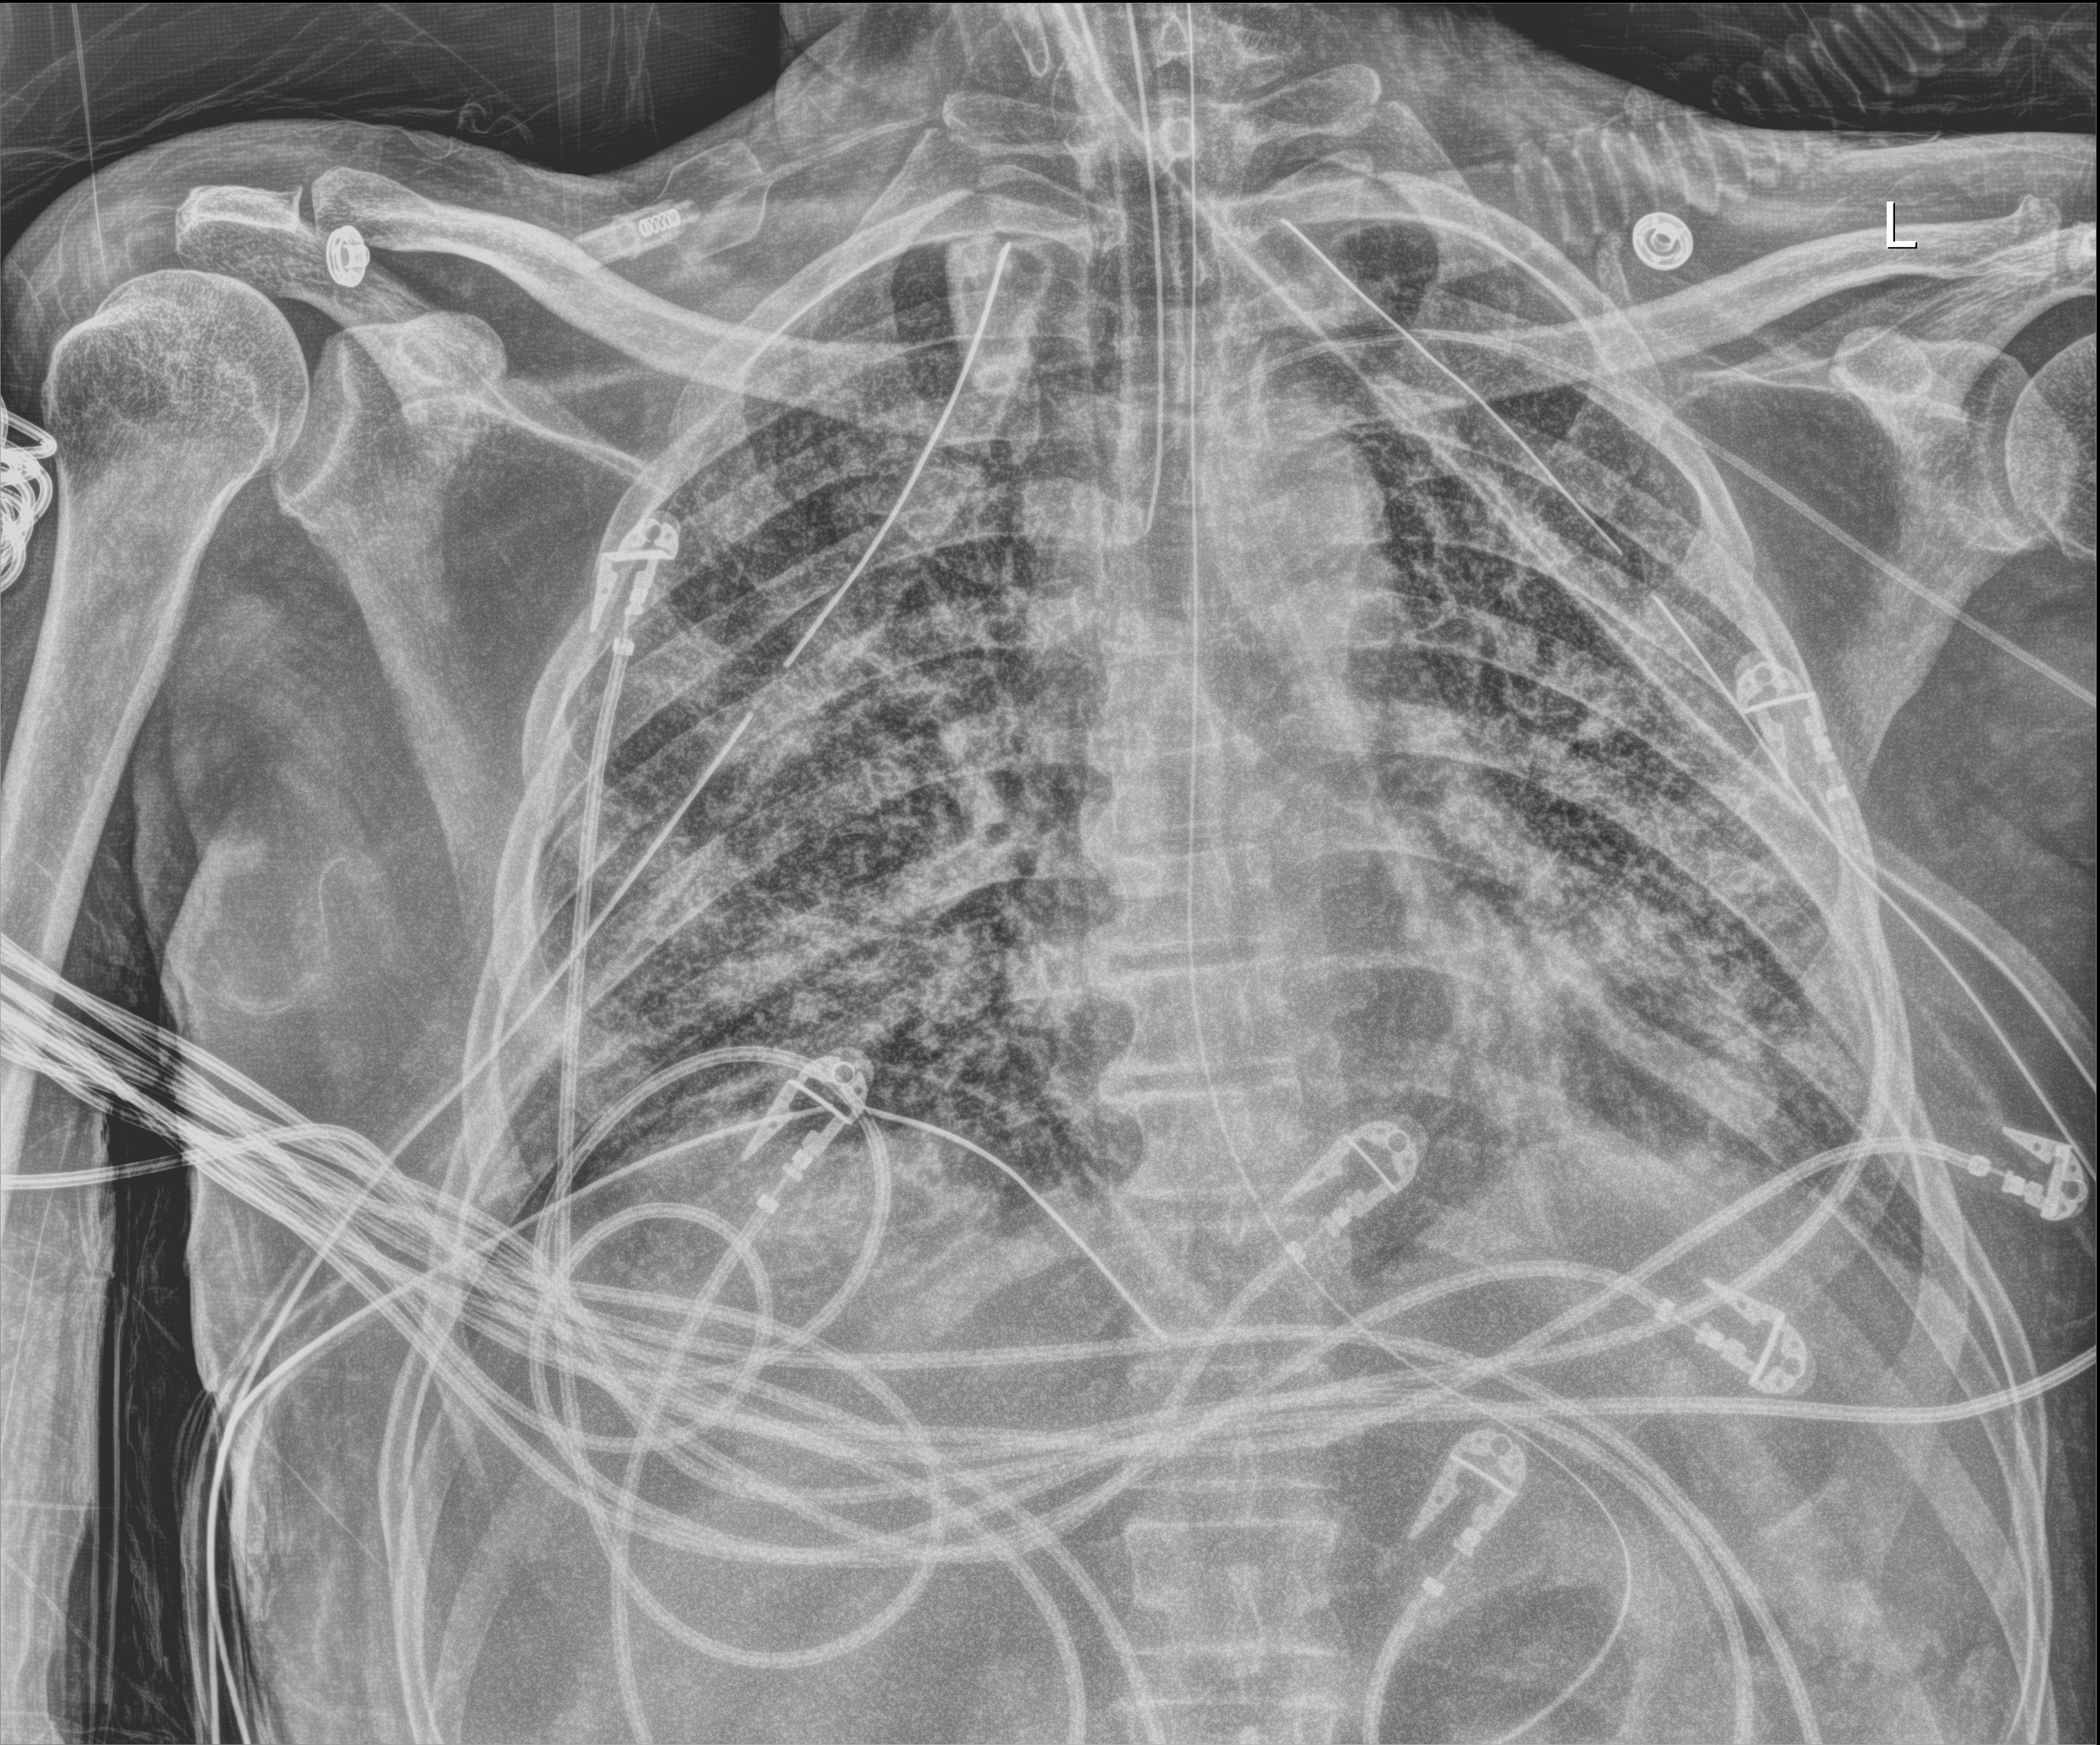
Chest X-ray (portable); anteroposterior (AP) projection. Patient hospitalised with COVID-19; male, aged 18–59 years.
Hospital-stay facts (about this admission, not read from this image; timing relative to this image not recorded):
- COPD (admission record): no